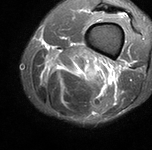
MRI of an extremity soft-tissue mass, one axial slice. Position 20 of 90 along the scan axis. STIR. MR volume resampled by the dataset authors to the PET/CT grid (not the native acquisition matrix). 3.27 mm slice thickness. 152 × 150 image matrix, field of view 148 × 146 mm. Male patient. Case-level facts recorded for this patient, not image findings: histological type: undifferentiated pleomorphic liposarcoma; grade: high; site of the primary tumour: left thigh.
Outlined on this slice (expert contour drawn on MRI and transferred to this co-registered scan by the dataset authors):
- gross tumour volume including surrounding oedema: box from (x=41, y=55) to (x=119, y=88) px